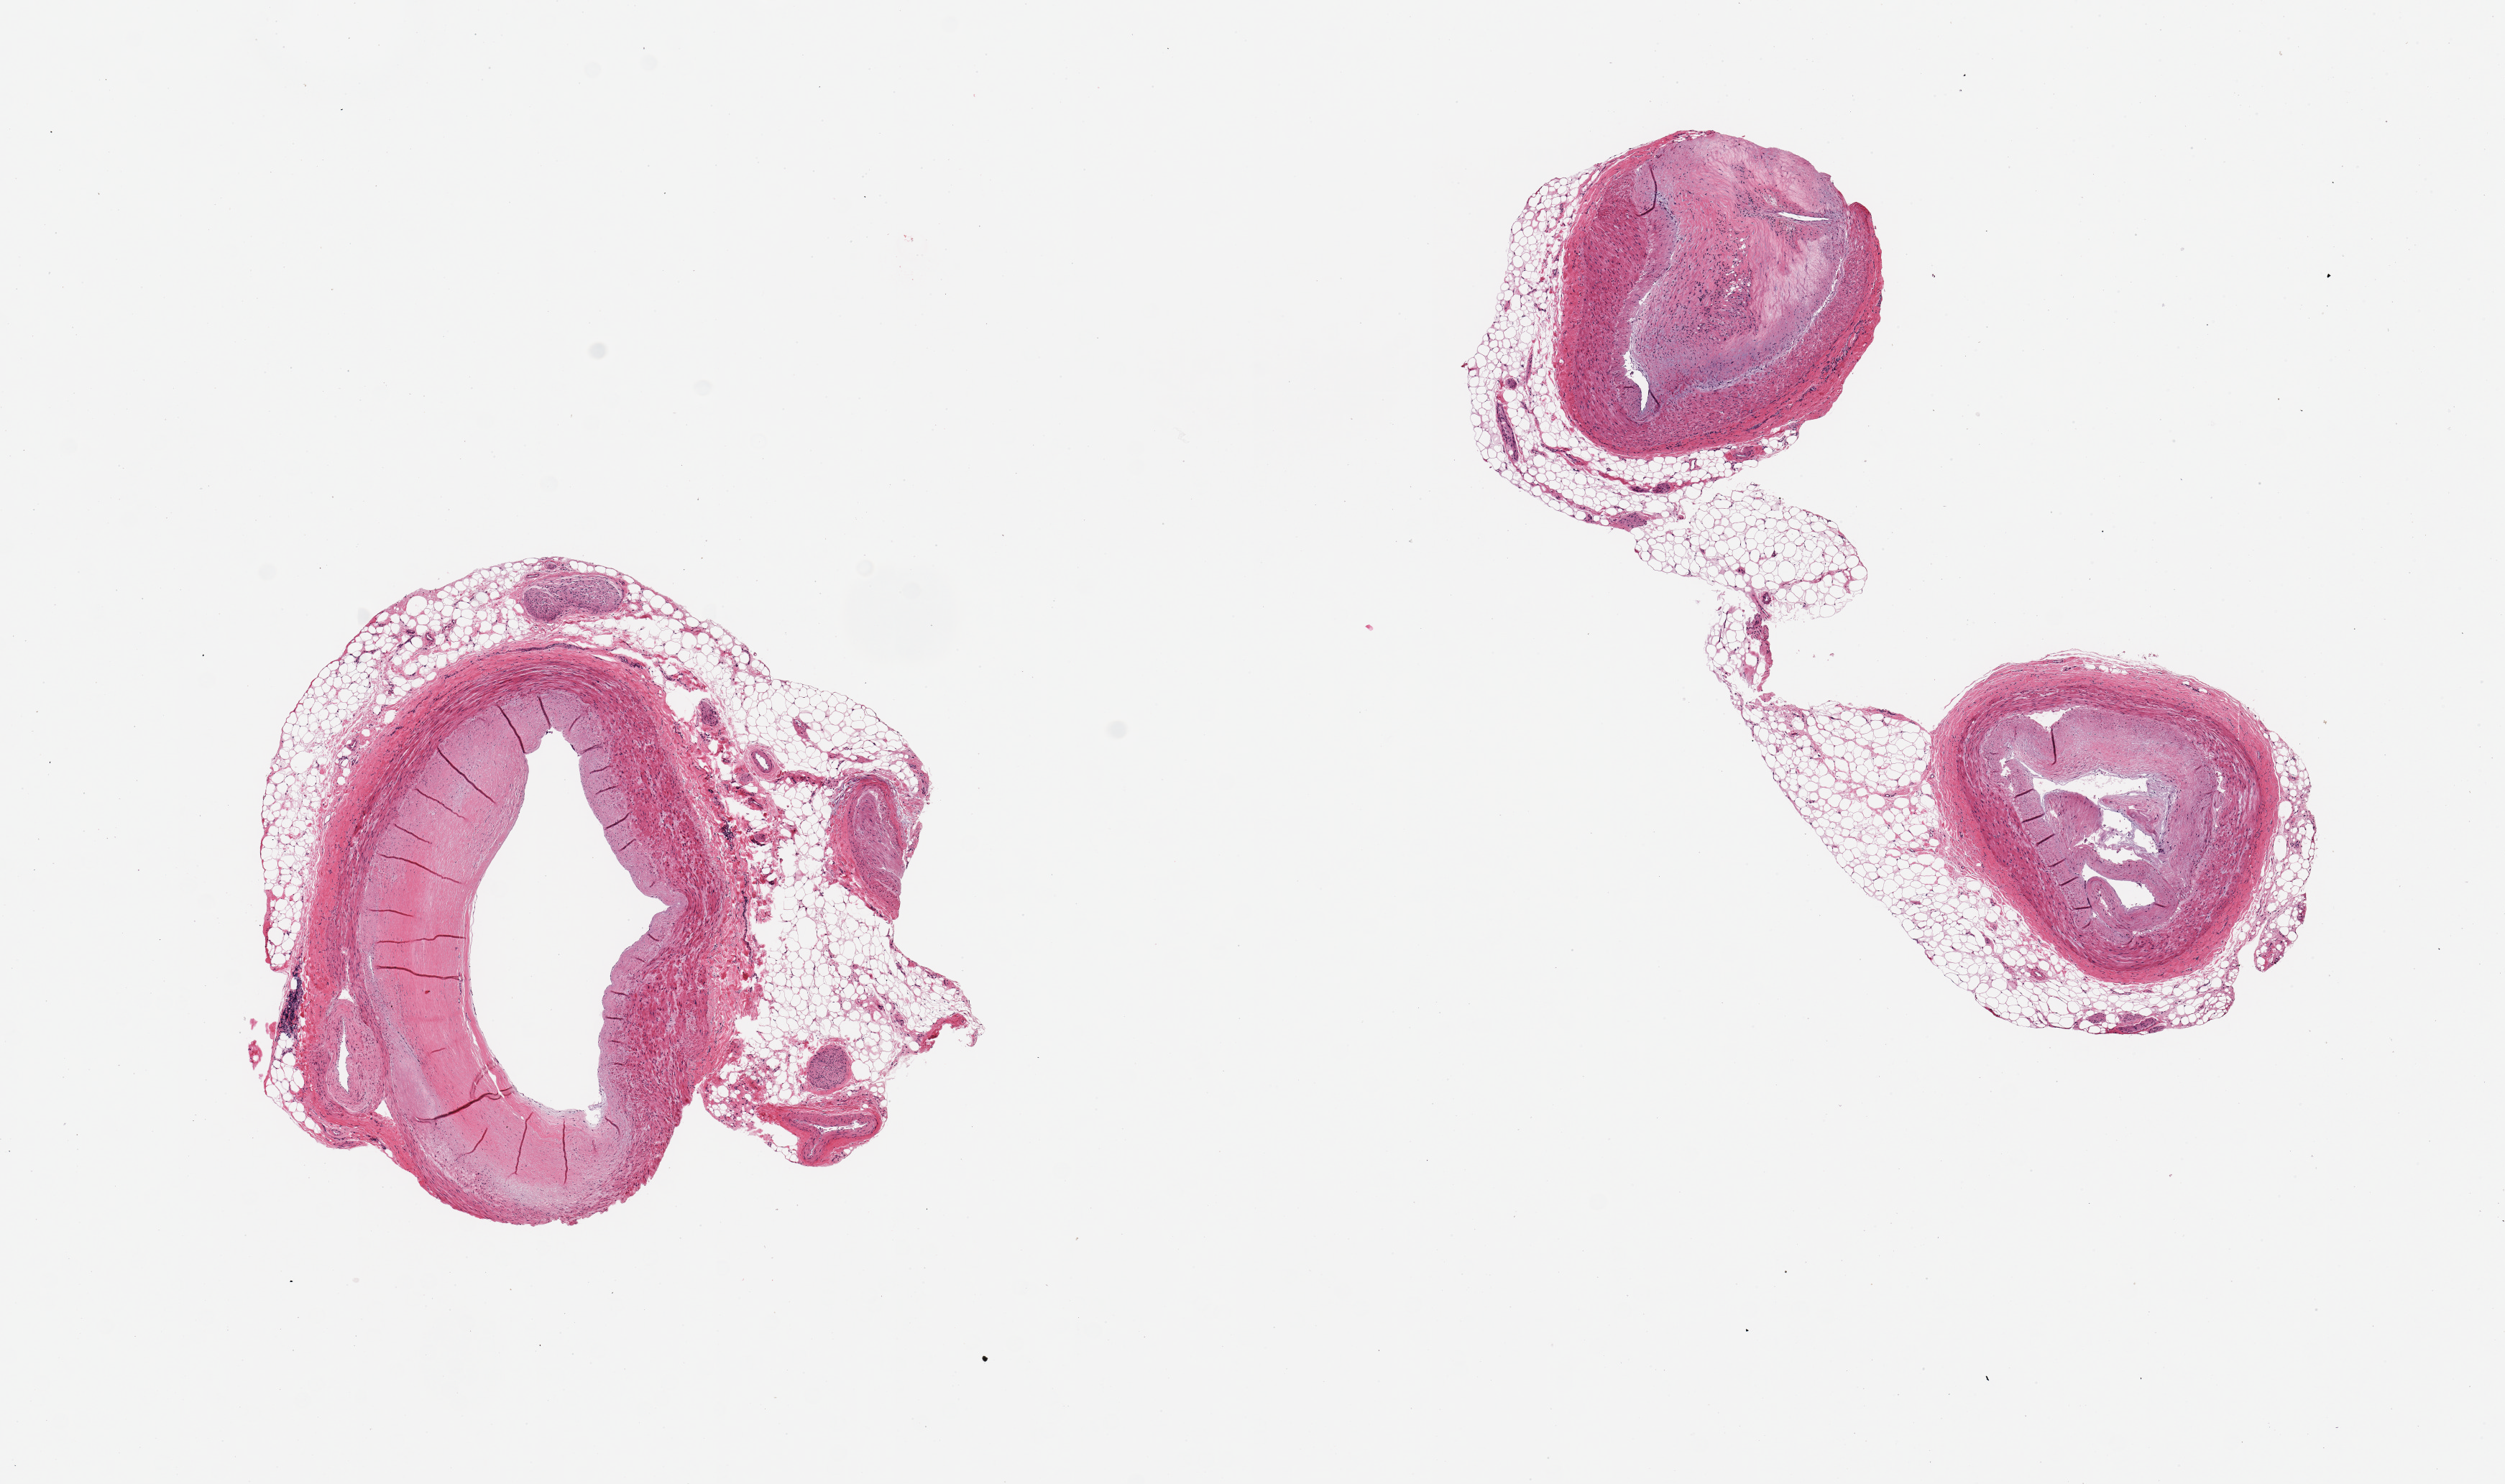
Digitized H&E-stained section, a low-resolution overview of the entire scanned area, about 13.8 x 8.2 mm; PAXgene-fixed, paraffin-embedded tissue; target tissue: coronary artery; tissue donor sample. Donor sex: female.
Pathologist's review note for this sample: 3 pieces, rim of adherent fat up to ~1mm; subtotally occlusvie atherosis.